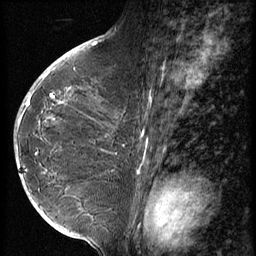
Breast MRI (dynamic contrast-enhanced), one sagittal slice. Position 33 of 56 along the scan axis. 3 images stored at this slice position (order not interpretable as contrast timing). 1.5 T. TE 4.2 ms, TR 9 ms. 2.5 mm slice thickness. 256 × 256 image matrix. Patient: female, 49 years. From the clinical record (not read from this slice): setting: breast cancer imaged before/during neoadjuvant chemotherapy; receptor status: HER2-positive.
Outlined on this slice (semi-automatically segmented with operator editing):
- analysis volume of interest (the breast-tissue region the enhancement analysis was run in; not a lesion): bounding box [x1, y1, x2, y2] px = [14, 79, 84, 203]
- tumour enhancement mask (voxels above the 140 % enhancement threshold inside the analysis volume of interest): [17, 147, 19, 165]